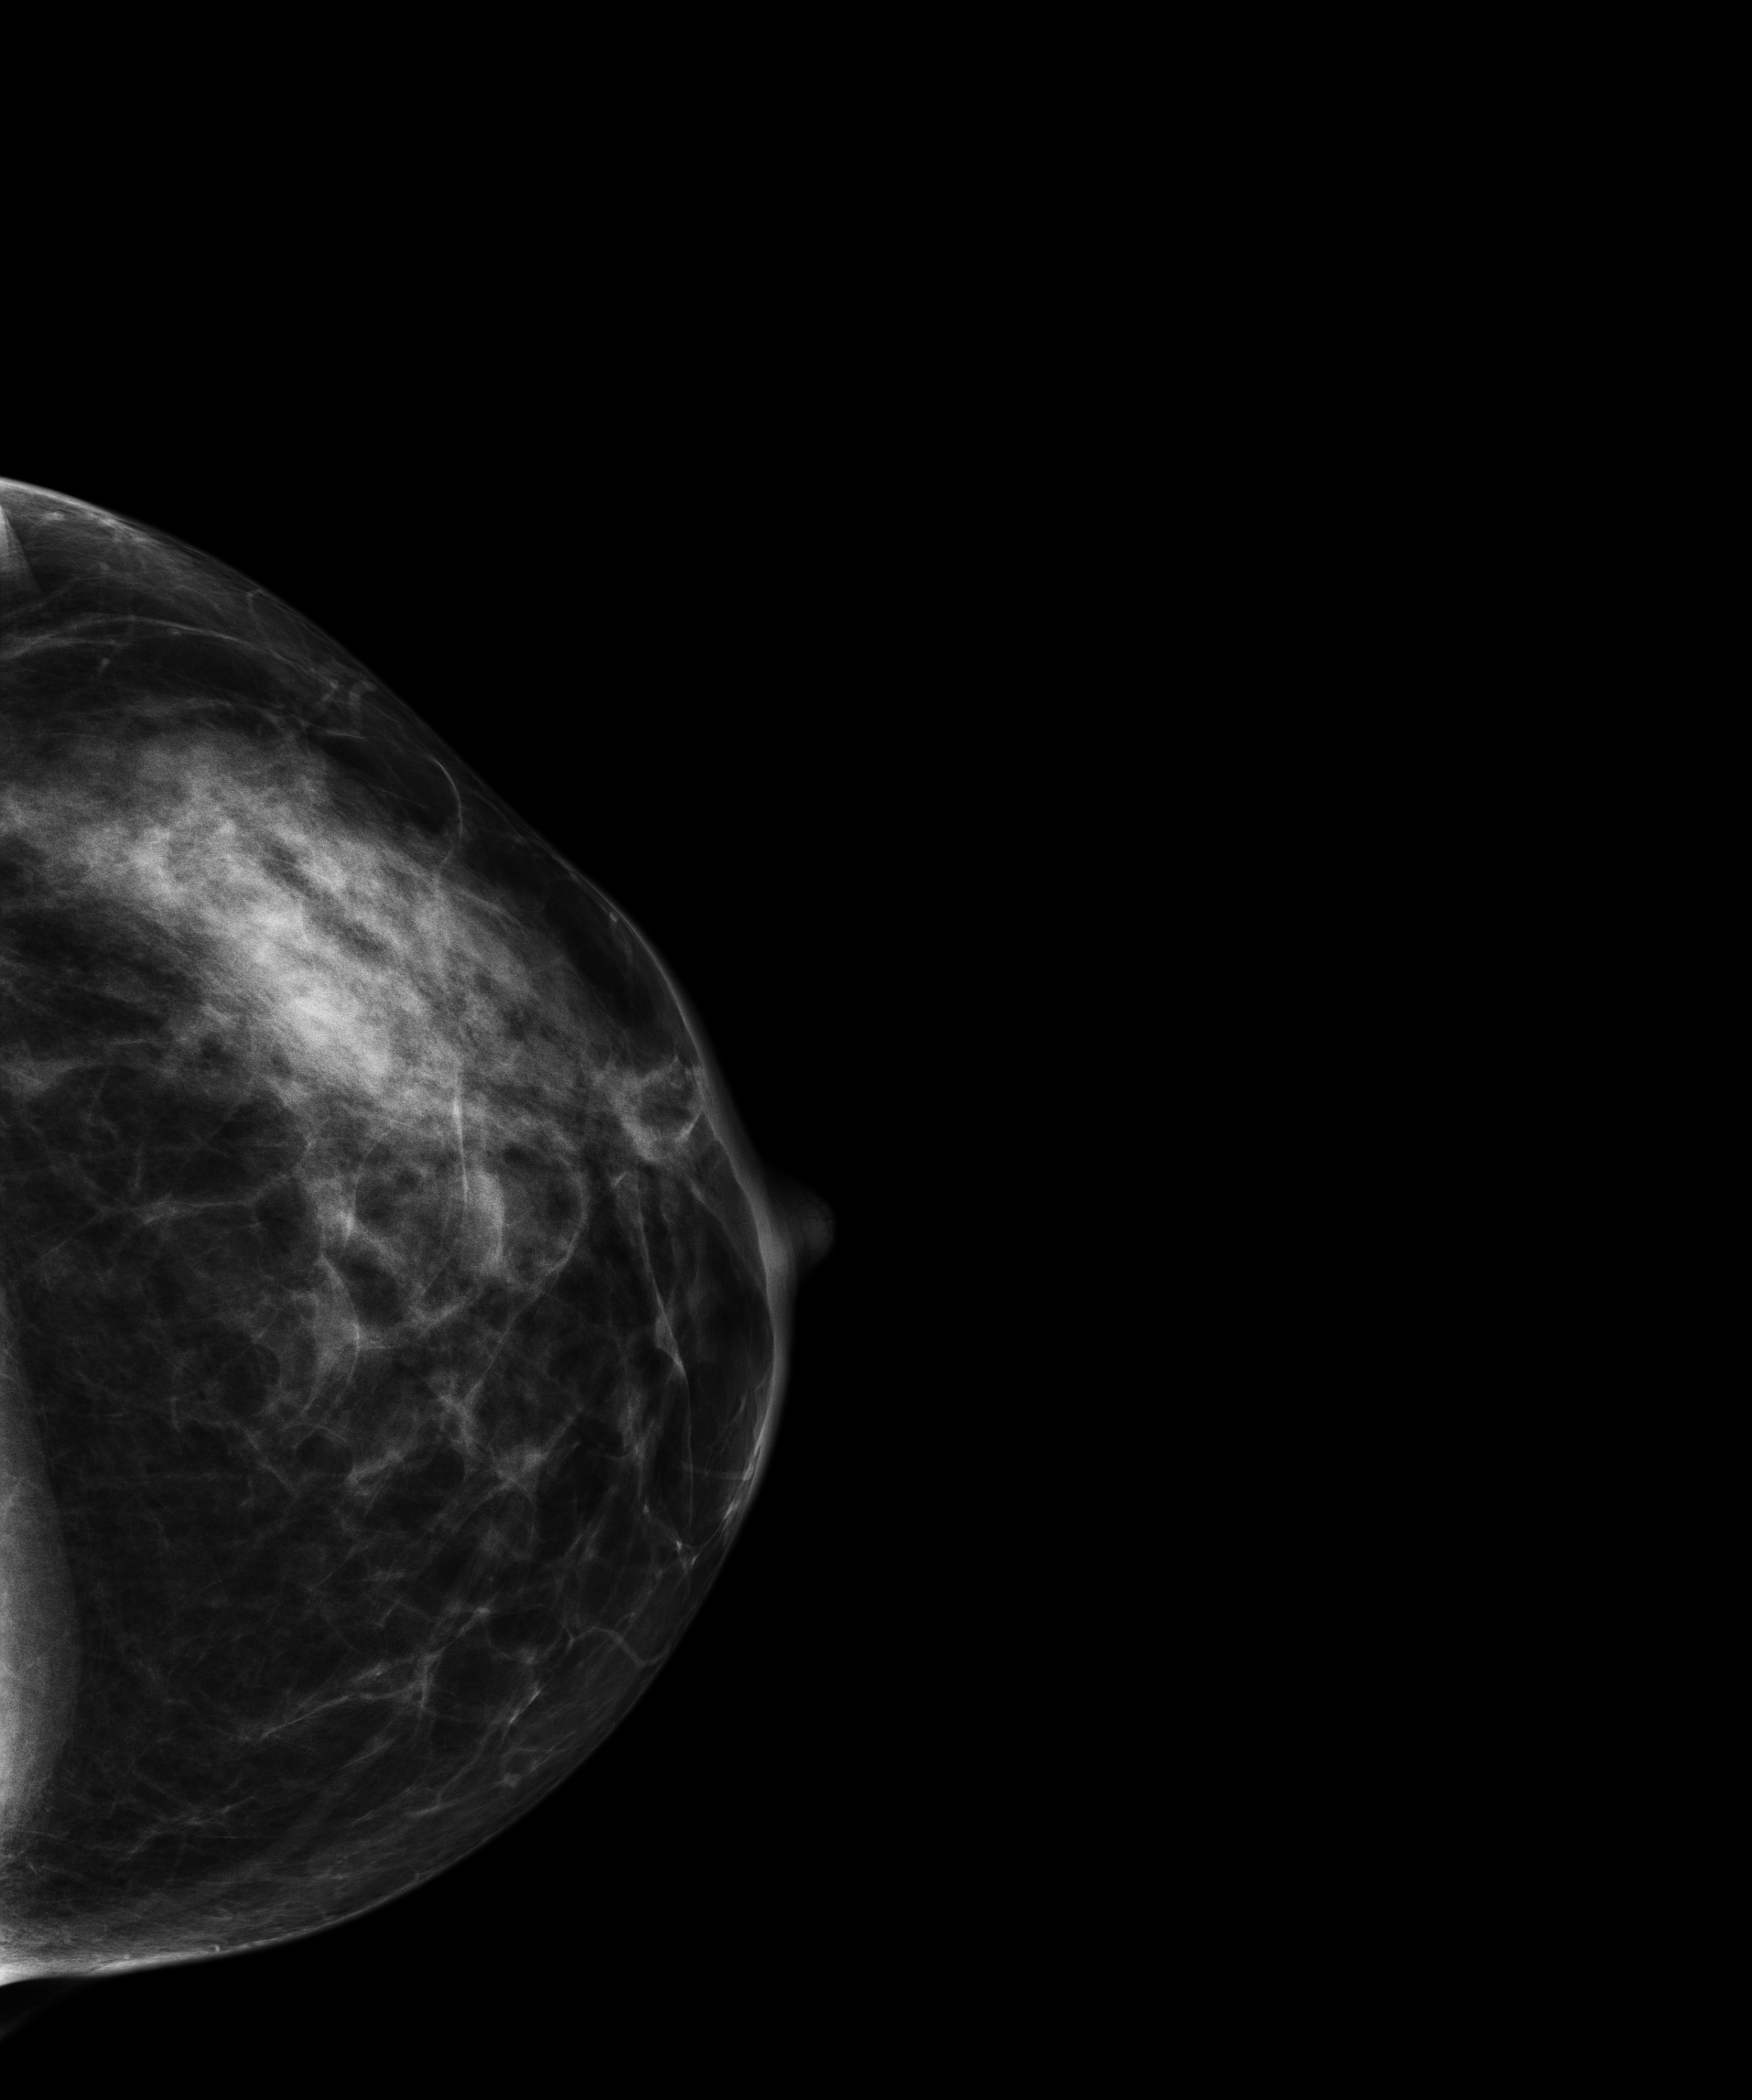
Full-field digital mammogram (FFDM); left breast; CC view; screening examination; compressed breast thickness 57 mm. Female patient, age 45 years.
Breast density at the screening exam (both breasts): heterogeneously dense (BI-RADS density category c). Final BI-RADS assessment for this screening round (tomosynthesis exam, both breasts): category 1. Recall: no recall after this screen.